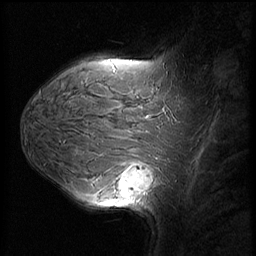
Breast MRI (dynamic contrast-enhanced), one sagittal slice. Slice 42 of 60 in the series (ordered by position). Dynamic contrast-enhanced series, image 2 of 3 at this slice position (ordered by acquisition). 1.5 T. TE 4.2 ms, TR 8.9 ms. 2.5 mm slice thickness. 256 × 256 image matrix, field of view 220 × 220 mm. Female patient, age 37 years. From the clinical record (not read from this slice): setting: breast cancer imaged before/during neoadjuvant chemotherapy; receptor status: triple-negative.
Annotated regions visible in this slice (semi-automatic segmentation, software-assisted and operator-edited):
- analysis volume of interest (the breast-tissue region the enhancement analysis was run in; not a lesion): bounding box [x1, y1, x2, y2] px = [114, 153, 159, 206]
- tumour enhancement mask (voxels above the 140 % enhancement threshold inside the analysis volume of interest): [120, 166, 153, 197]